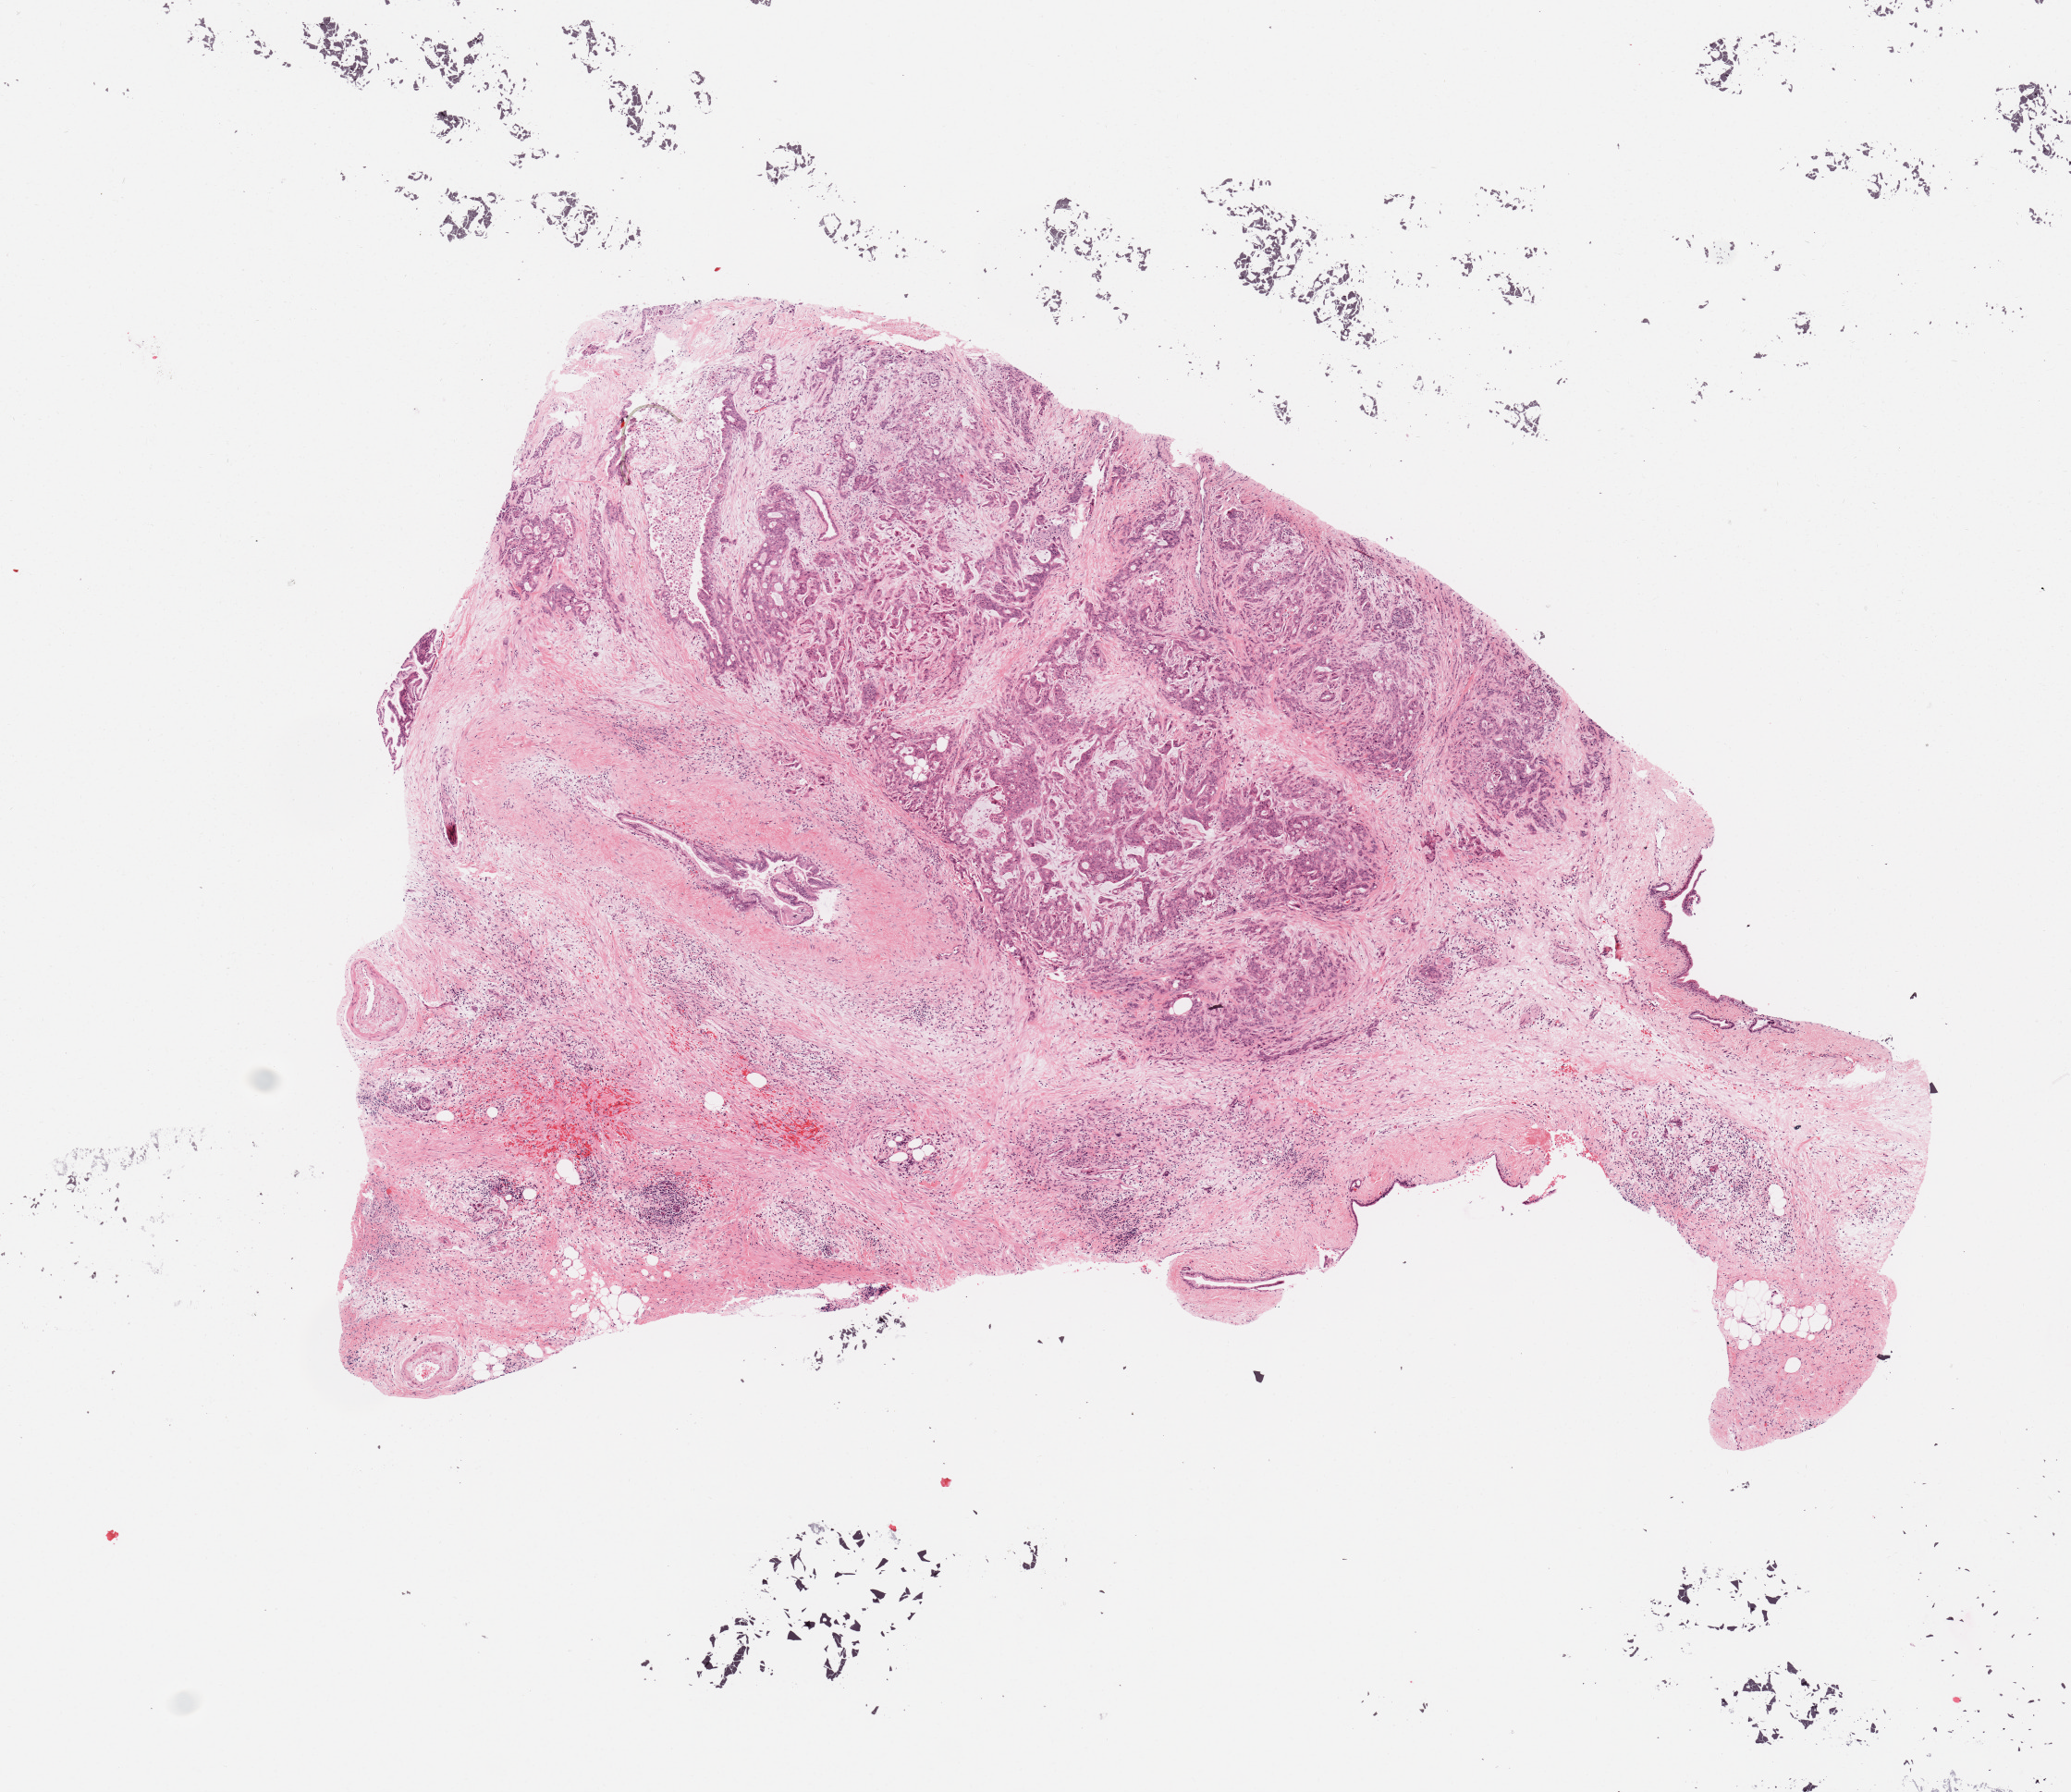
Whole-slide histology image, Hematoxylin and eosin (H&E) stained, low-resolution overview of the scanned area, about 8.9 x 7.7 mm. Tumour tissue sample, sampled site: pancreas. 65-year-old male patient. Histologic grade: G3 (poorly differentiated). Composition of this section per pathologist review: tumour nuclei 60%, necrosis 2%.
AJCC pathologic stage: IA. Histologic diagnosis: Infiltrating duct carcinoma, NOS.